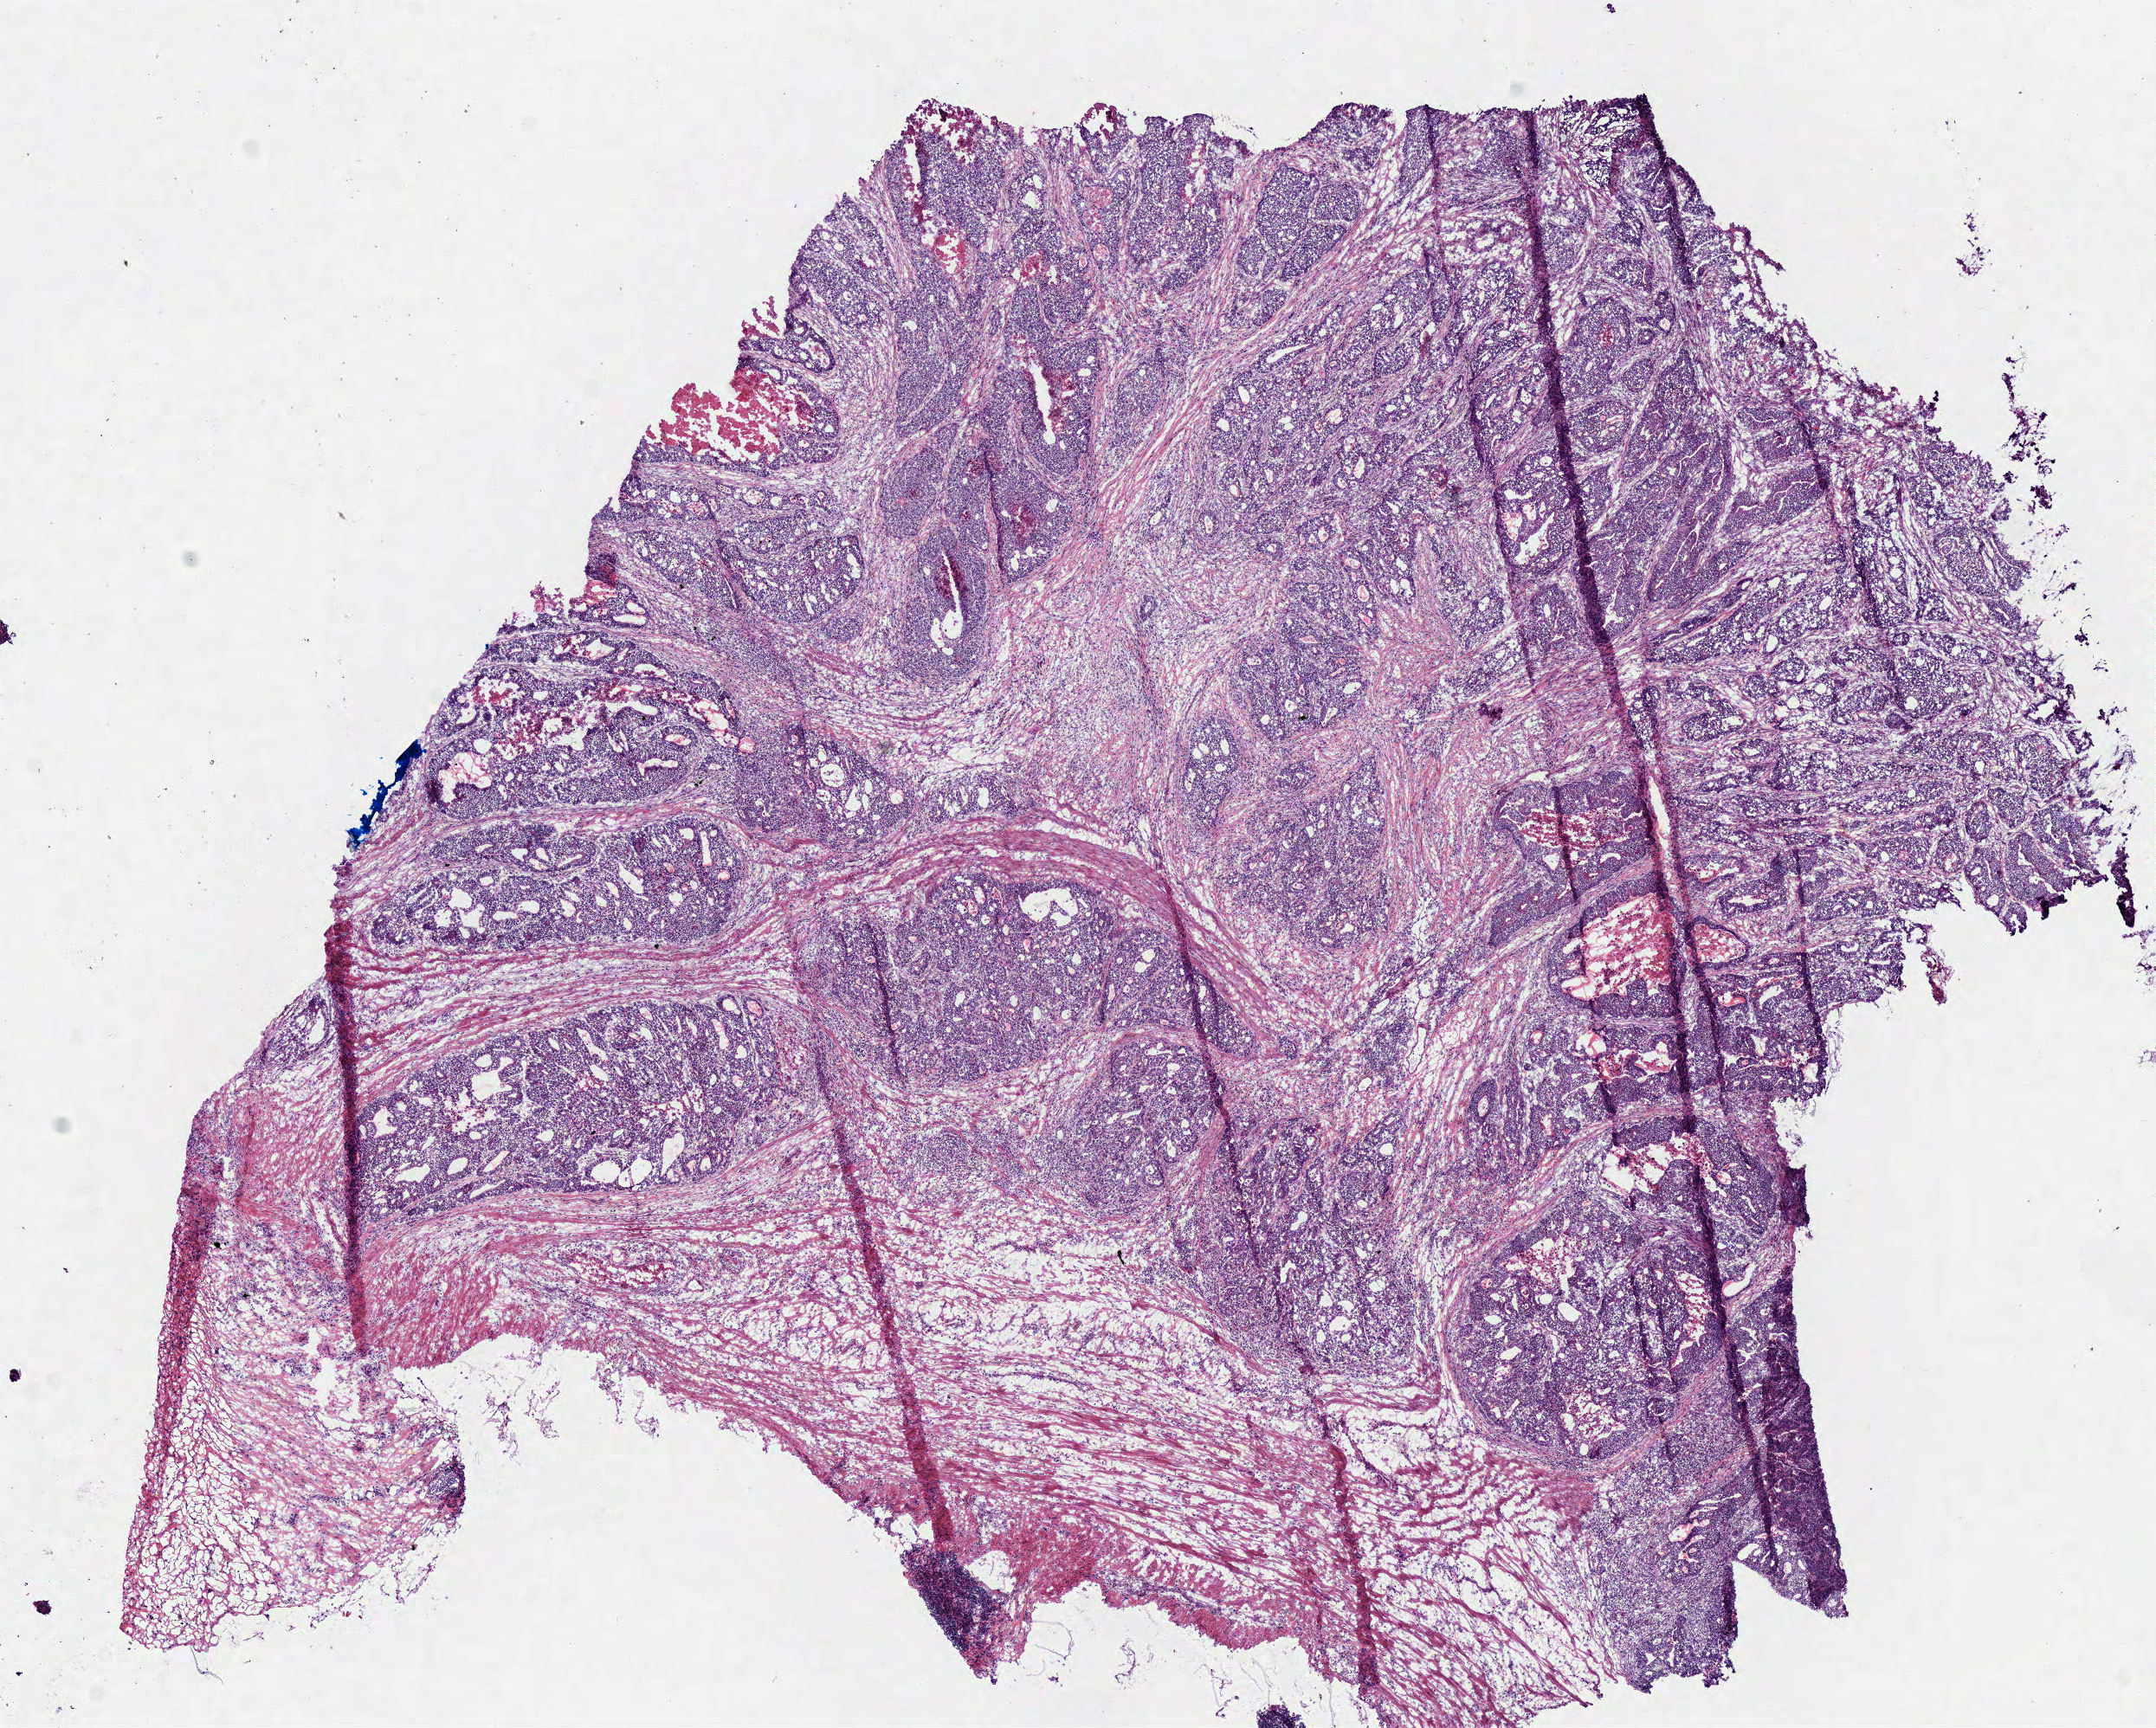
Hematoxylin and eosin (H&E) stained whole-slide image — whole scanned area (about 9.8 x 7.8 mm, acquisition: 40x scan) shown as a low-resolution overview; frozen section; primary tumour sample from the colon. Male, age 75 years at initial diagnosis. Composition of this section per pathologist review: tumour cells 95%, tumour nuclei 80%.
Histologic diagnosis: Adenocarcinoma, NOS (hepatic flexure of colon).